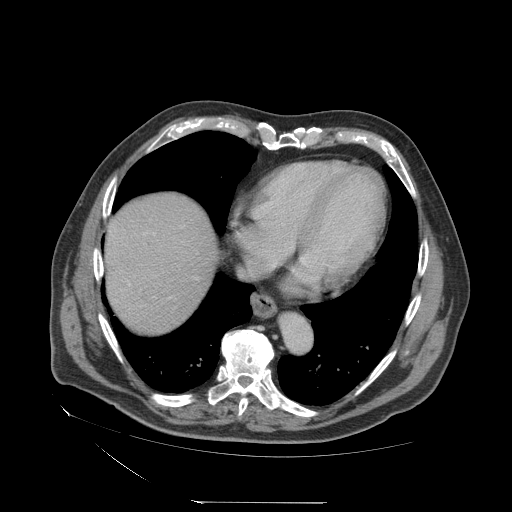
Contrast-enhanced abdominal CT (liver protocol), one axial slice. Slice 67 of 83 in the series (ordered by position). Reconstruction kernel STANDARD. 140 kVp. Soft-tissue window (W 400 / L 40 HU). 2.5 mm slice thickness. 512 × 512 image matrix. Case-level facts recorded for this patient, not image findings: diagnosis: hepatocellular carcinoma (patient treated with transarterial chemoembolisation; whether this scan precedes or follows treatment is not stated here); TNM stage (as recorded): Stage-I; Child-Pugh class: A.
Structures marked on this image (semi-automatic segmentation, software-assisted and operator-edited):
- liver parenchyma outside the tumour (the mass and vessels are separate outlines, so this box may not span the whole liver): bounding box [x1, y1, x2, y2] px = [104, 194, 217, 332]